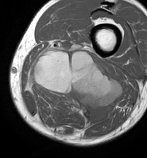
MRI of an extremity soft-tissue mass, one axial slice. Slice 33 of 86 in the series (ordered by position). MR volume resampled by the dataset authors to the PET/CT grid (not the native acquisition matrix). 3.27 mm slice thickness. 147 × 158 image matrix, field of view 144 × 154 mm. Male patient. Case-level facts recorded for this patient, not image findings: histological type: undifferentiated pleomorphic liposarcoma; grade: high; site of the primary tumour: left thigh.
Structures marked on this image (expert contour drawn on MRI and transferred to this co-registered scan by the dataset authors):
- gross tumour volume including surrounding oedema: bounding box <26,40,122,127> (left, top, right, bottom; pixels)
- gross tumour volume (mass): <30,51,120,123>